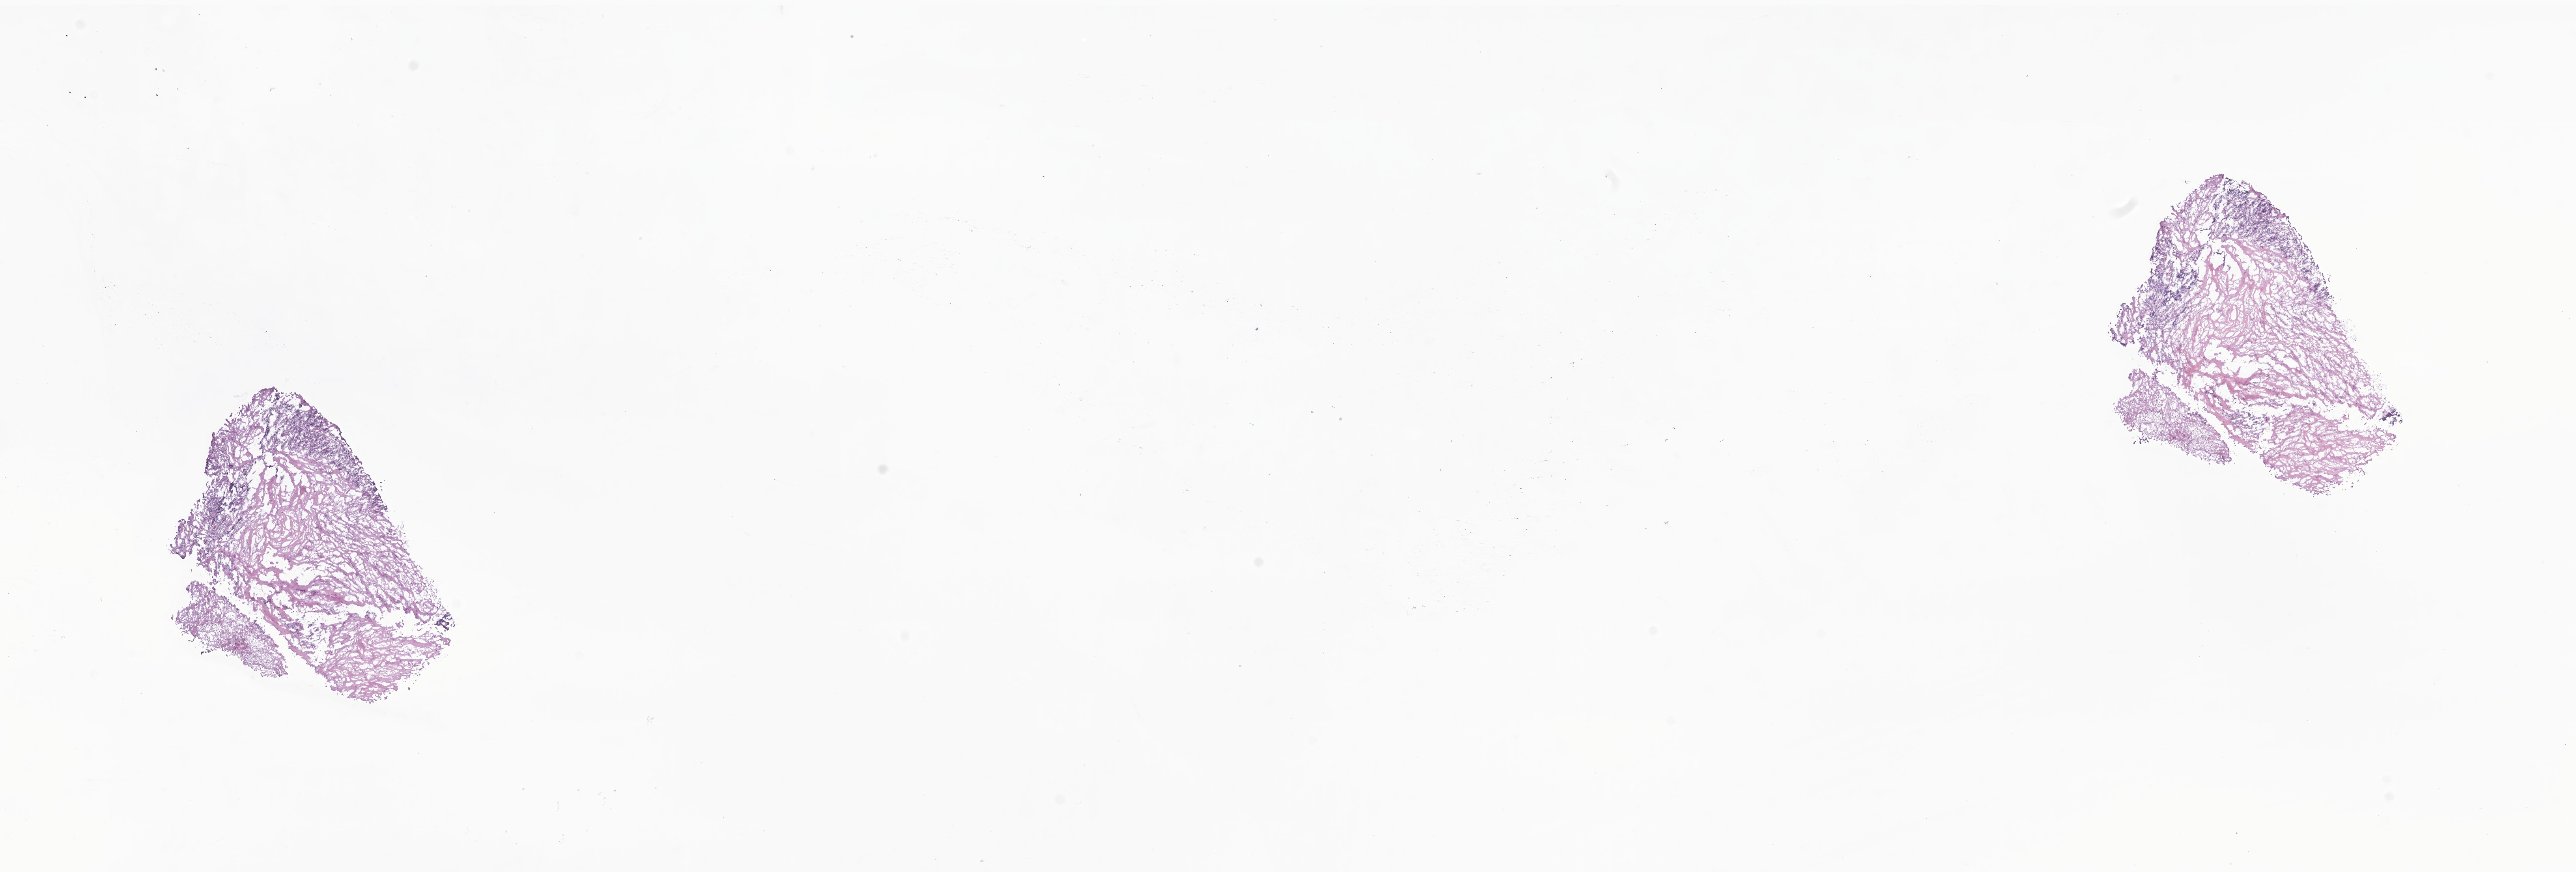
Digitized H&E-stained section of tumor tissue from the brain, low-resolution overview of the scanned area, about 27.5 x 9.3 mm. Cryosection (OCT / tissue freezing medium). Male patient, age 149 months.
Diagnosis: Medulloblastoma, NOS.